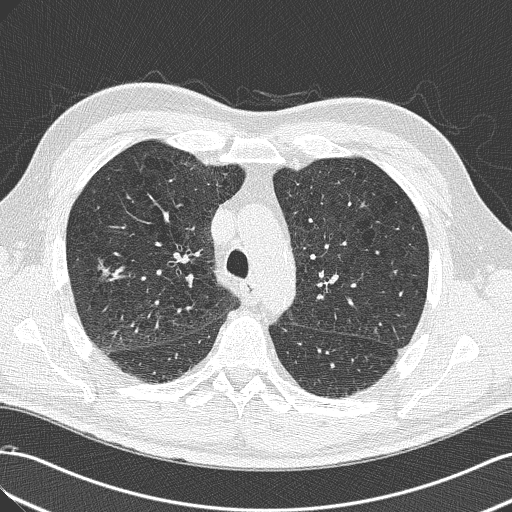
Low-dose screening chest CT, one axial slice. Position 96 of 143 along the scan axis. 120 kVp. Lung window (W 1500 / L -600 HU). 512 × 512 image matrix.
Annotated regions visible in this slice (expert manual segmentation):
- lesion 1 (tumor, lower lobe of right lung): bounding box <98,260,110,276> (left, top, right, bottom; pixels)